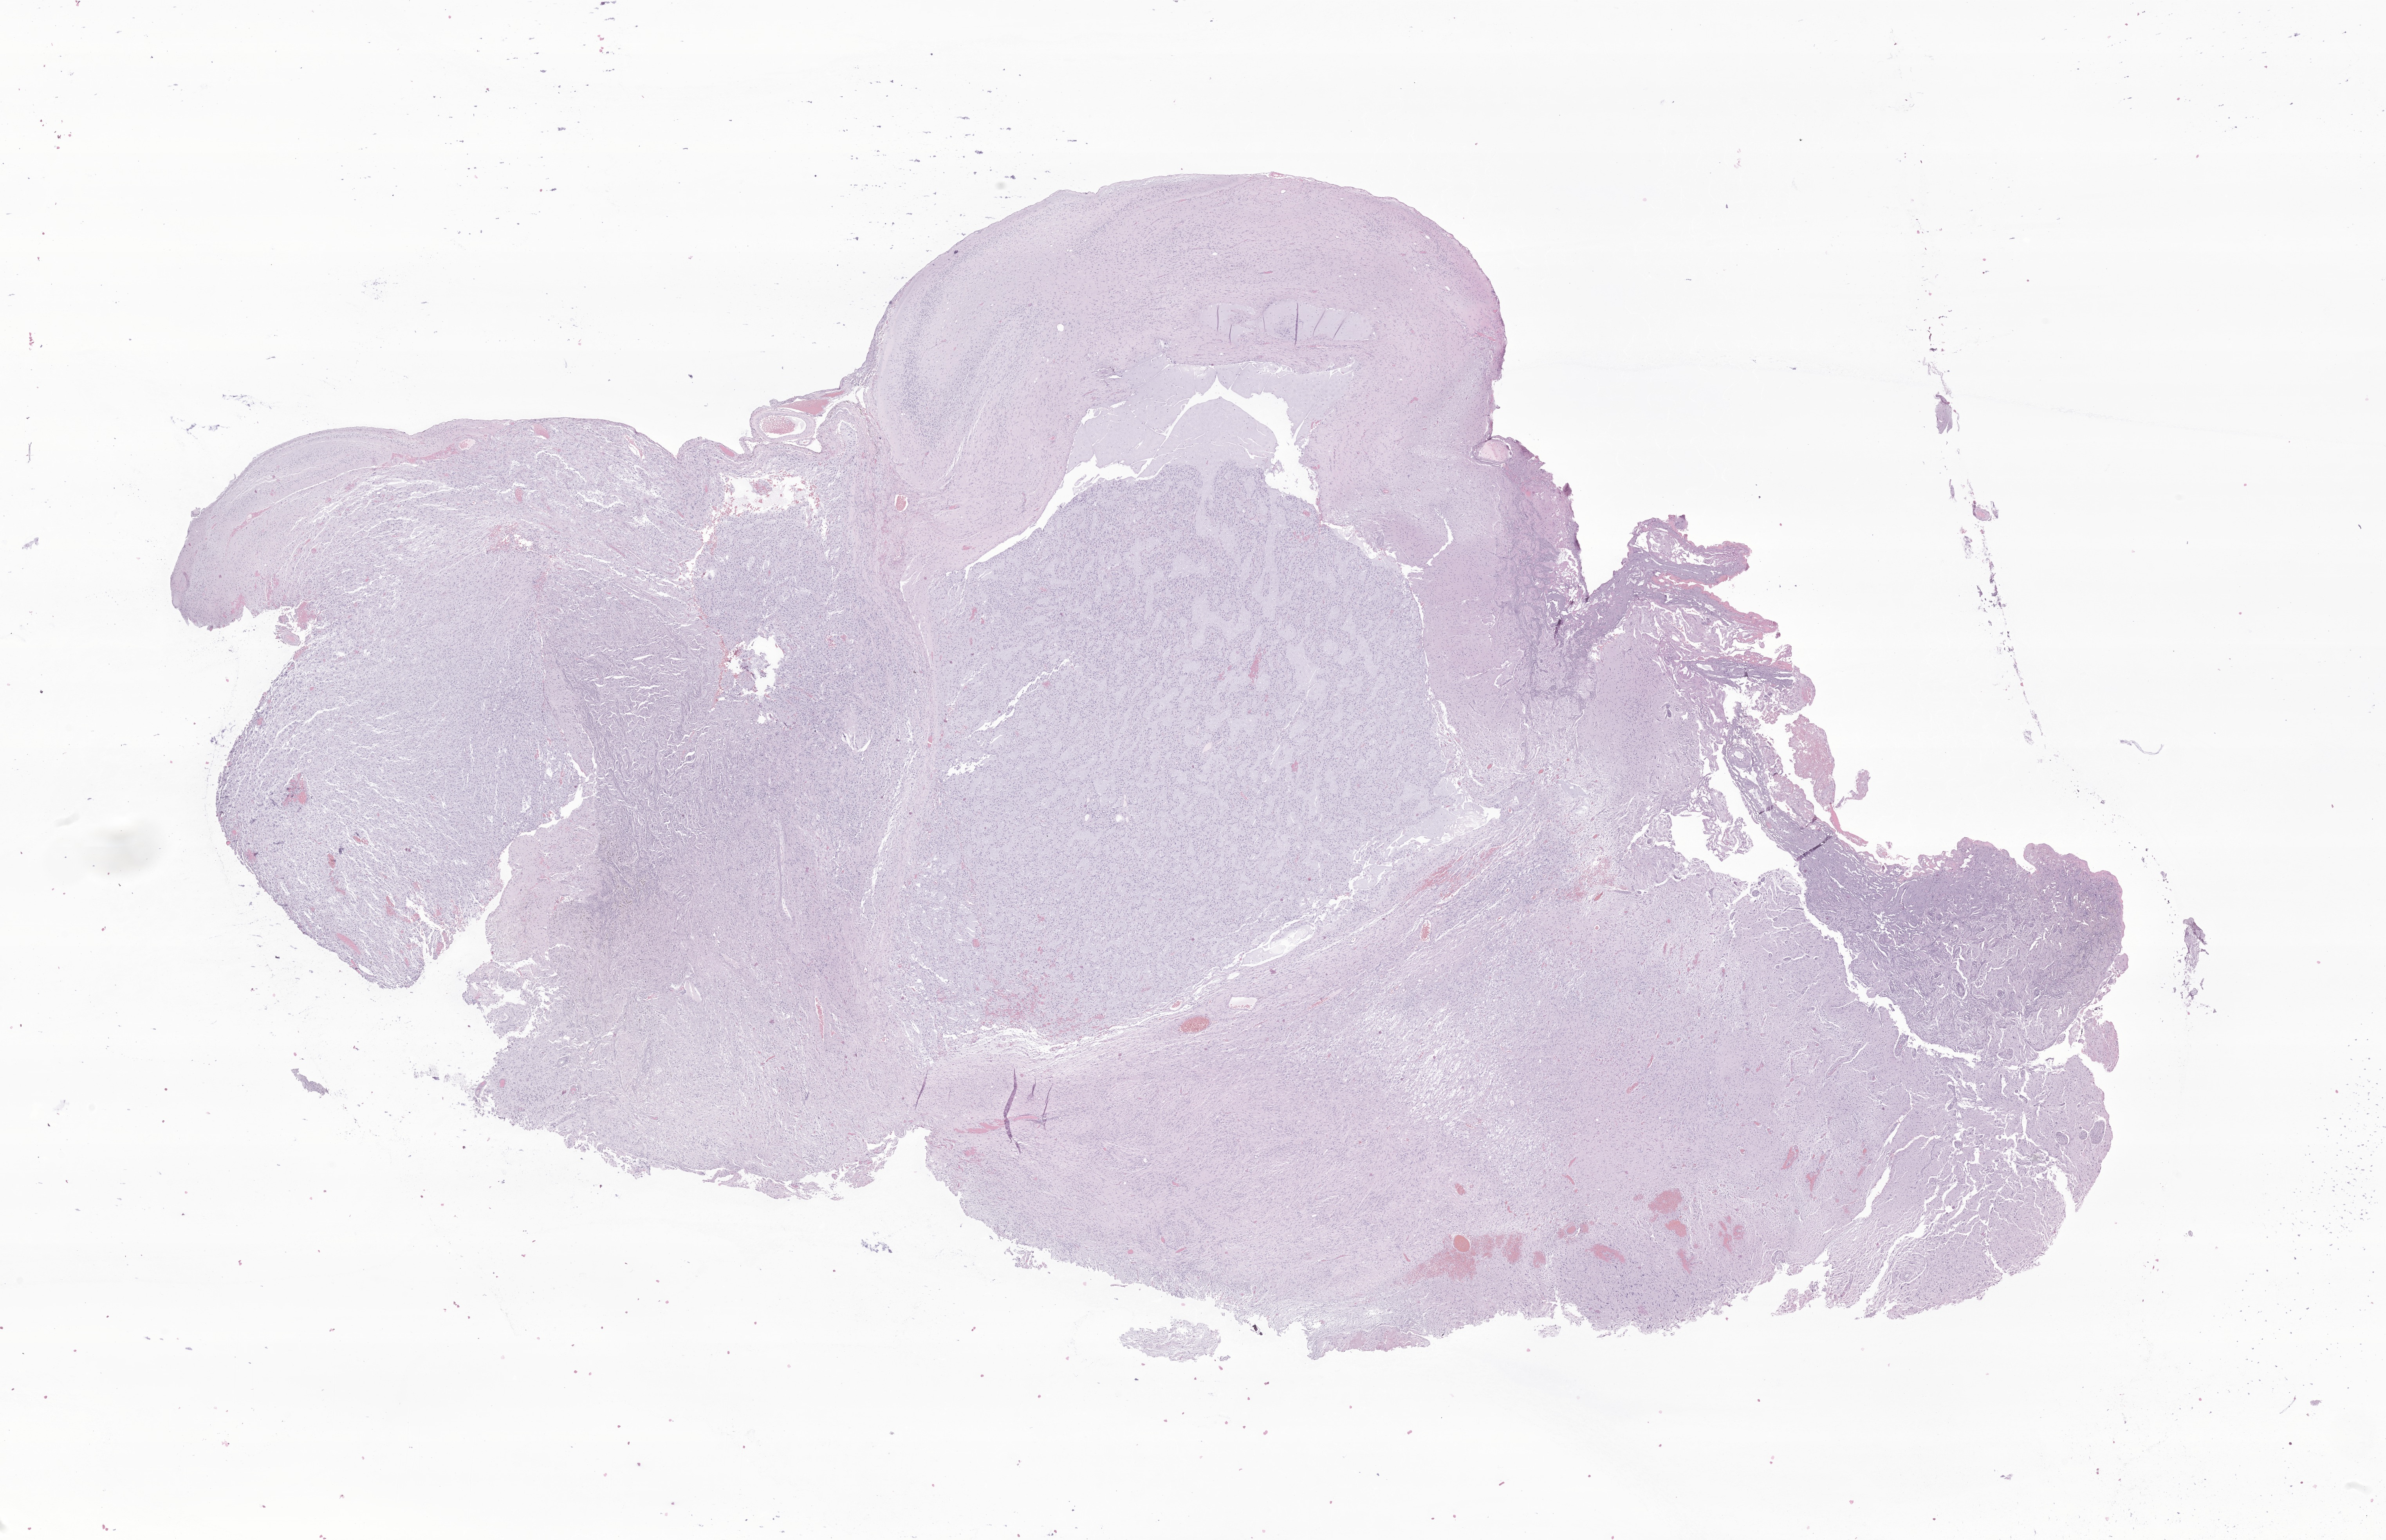
Whole-slide image, H&E stain of tumor tissue from the brain stem — whole scanned area (about 25.7 x 16.6 mm) shown as a low-resolution overview. Formalin-fixed, paraffin-embedded (FFPE) tissue. Female patient, age 212 months (17 years 8 months).
* diagnosis (ICD-O-3 morphology term): Pilocytic astrocytoma